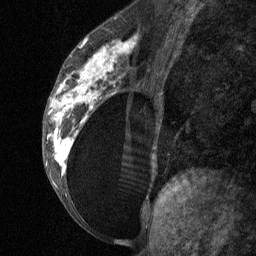
Breast MRI (dynamic contrast-enhanced), one sagittal slice. Slice 33 of 64 in the series (ordered by position). Dynamic contrast-enhanced study with each time point stored as its own series, time point 2 of 3 at this slice position (early post-contrast, ordered by acquisition time). 1.5 T. TE 4.8 ms, TR 27 ms. 256 × 256 image matrix, field of view 180 × 180 mm. Patient: female, 34 years. From the clinical record (not read from this slice): setting: breast cancer imaged before/during neoadjuvant chemotherapy; receptor status: HR-positive, HER2-negative.
Structures marked on this image (semi-automatically segmented with operator editing):
- analysis volume of interest (the breast-tissue region the enhancement analysis was run in; not a lesion): box from (x=42, y=23) to (x=157, y=197) px
- tumour enhancement mask (voxels above the 90 % enhancement threshold inside the analysis volume of interest): (x=48, y=36)–(x=136, y=176)